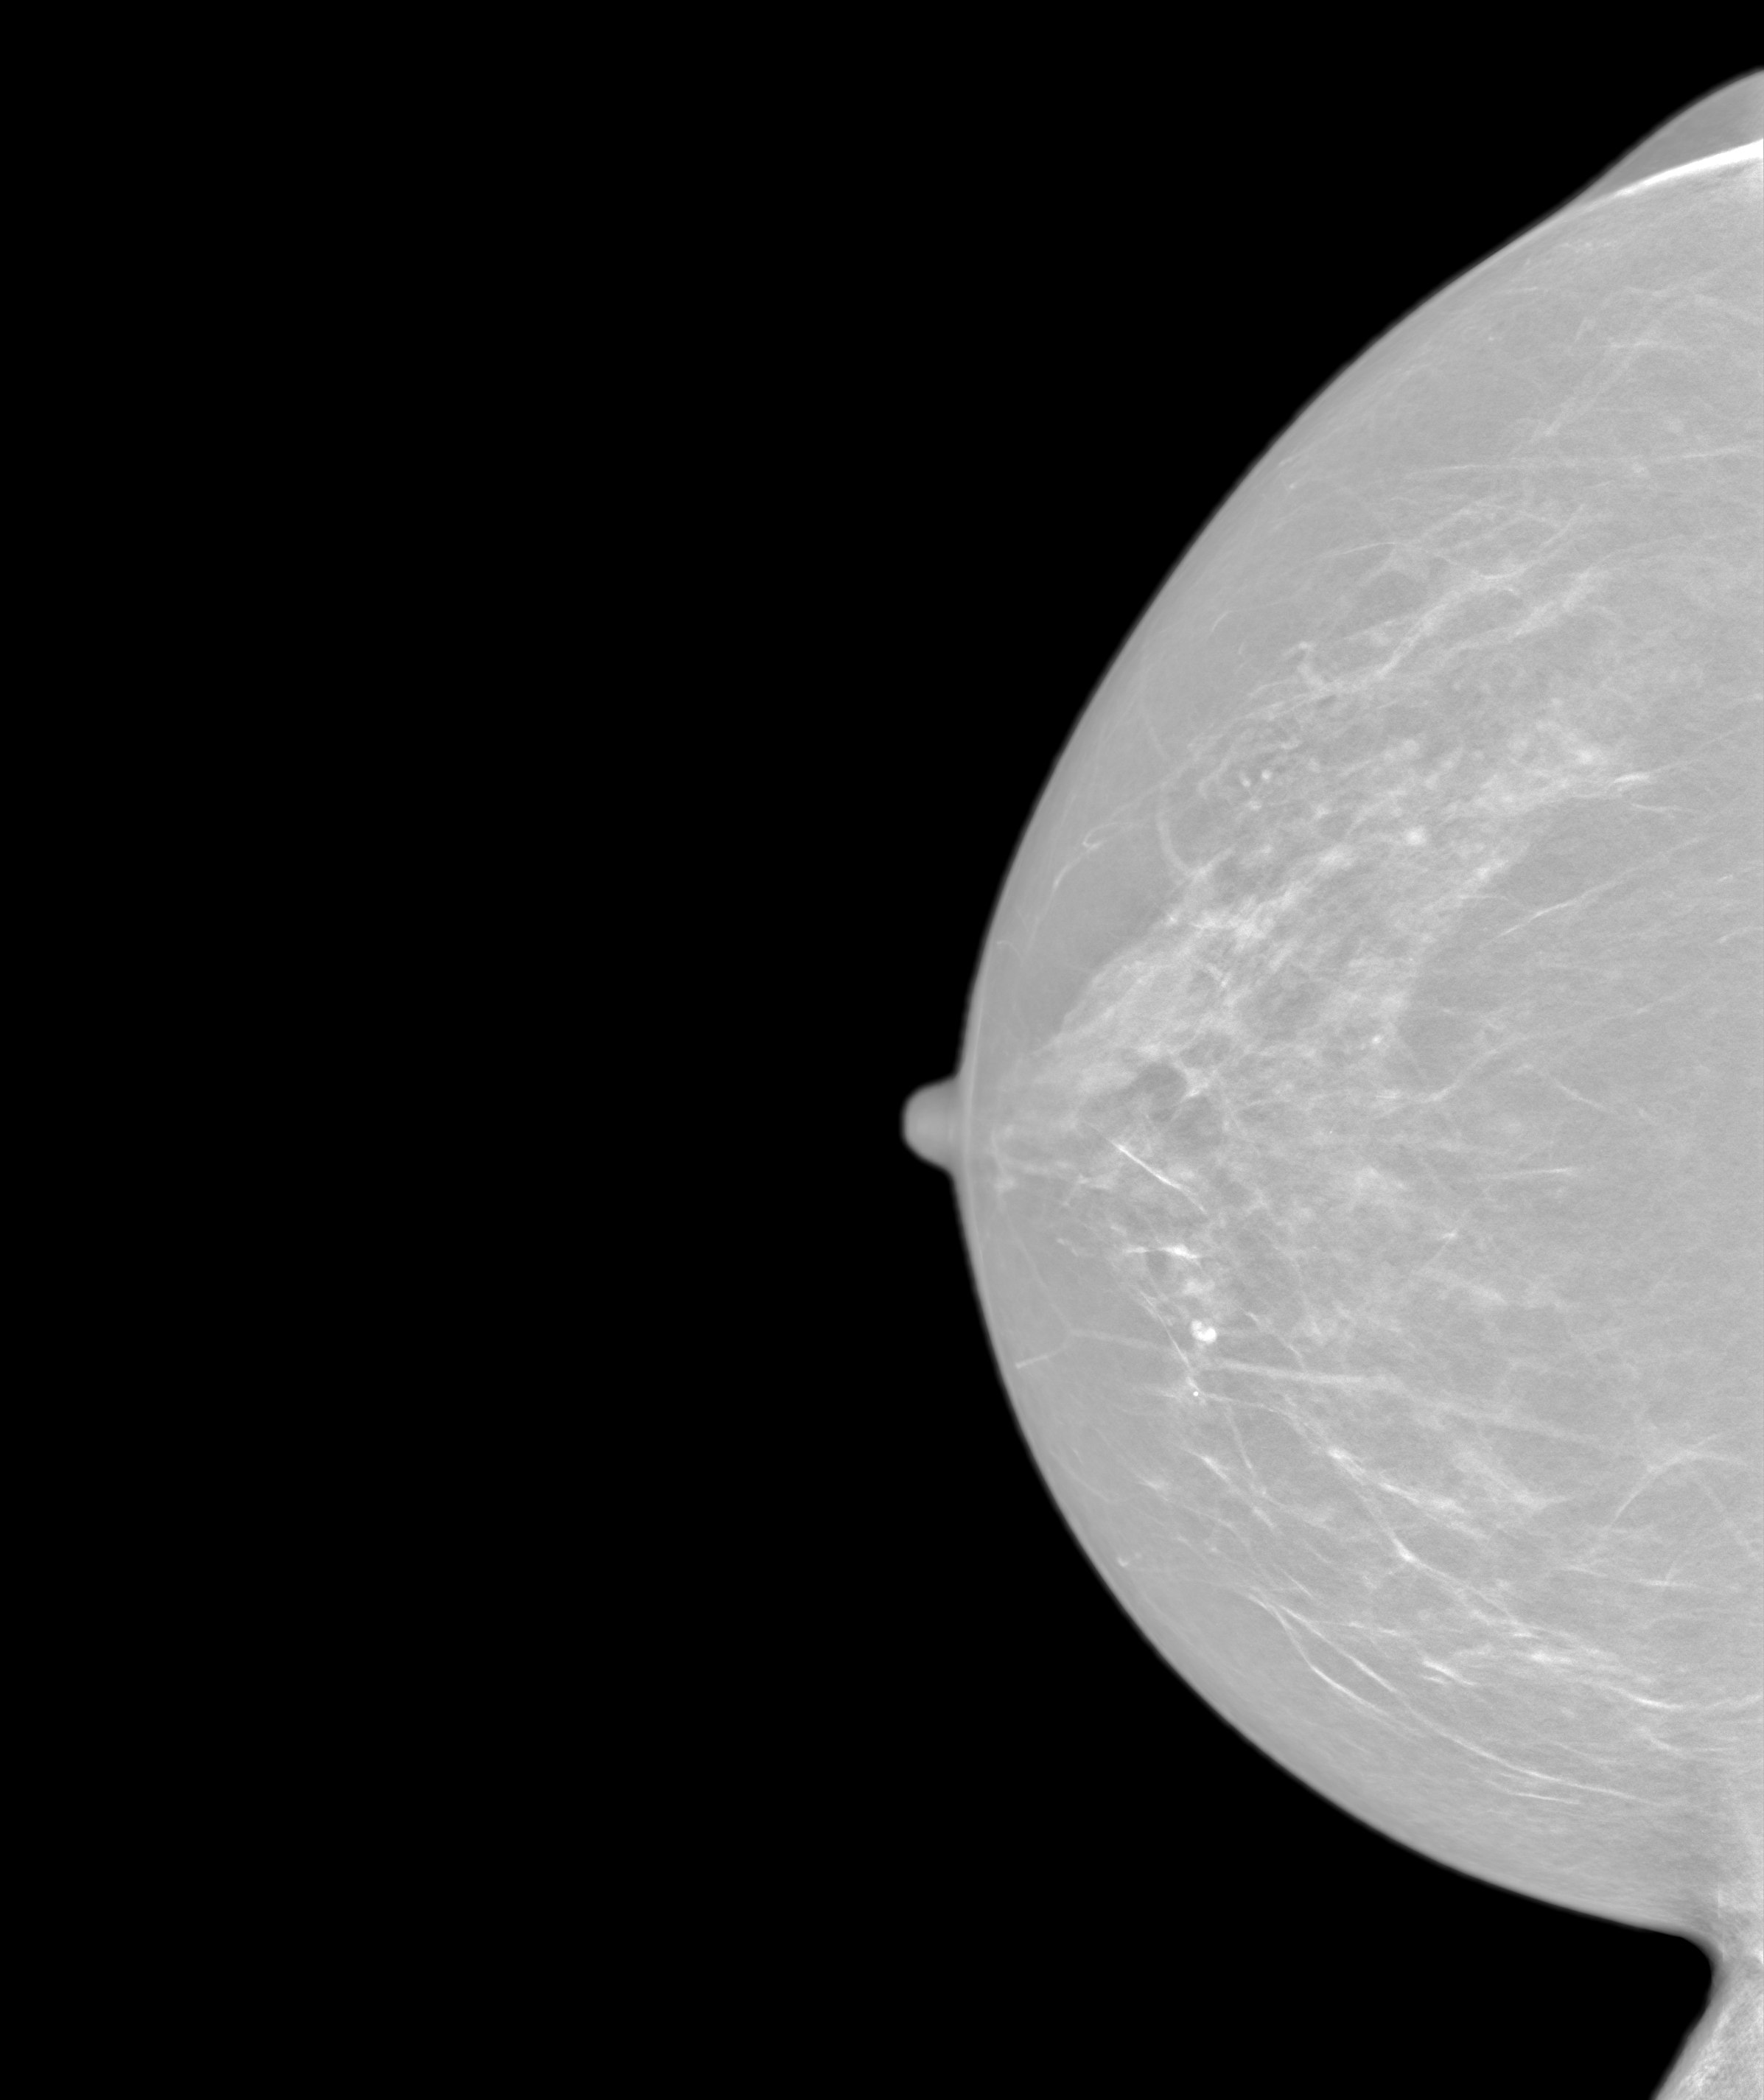
Screening examination. Female patient, age 54 years.
Image type: synthesized 2-D view from tomosynthesis. Breast: right. Projection: craniocaudal (CC) view.